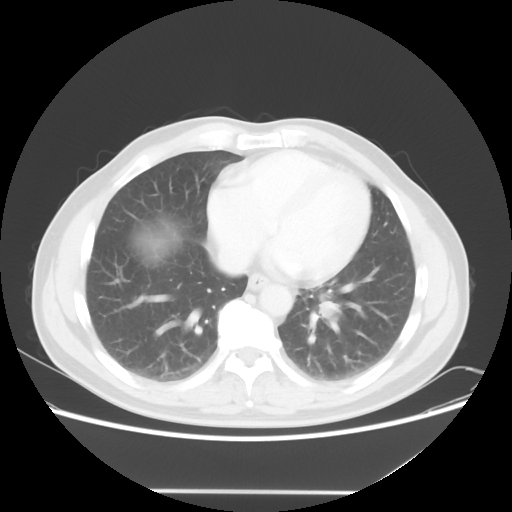
Chest CT, one axial slice. Slice 20 of 56 in the series (ordered by position). Reconstruction kernel STANDARD. 120 kVp. Lung window (W 1500 / L -600 HU). 5 mm slice thickness. 512 × 512 image matrix, field of view 385 × 385 mm. Patient: male, 61 years. From the clinical record (not read from this slice): clinical TNM (as recorded): T1c N0 M0.
Outlined on this slice (bounding box drawn by a radiologist):
- lung tumour (recorded histology: adenocarcinoma): box from (x=313, y=293) to (x=342, y=321) px